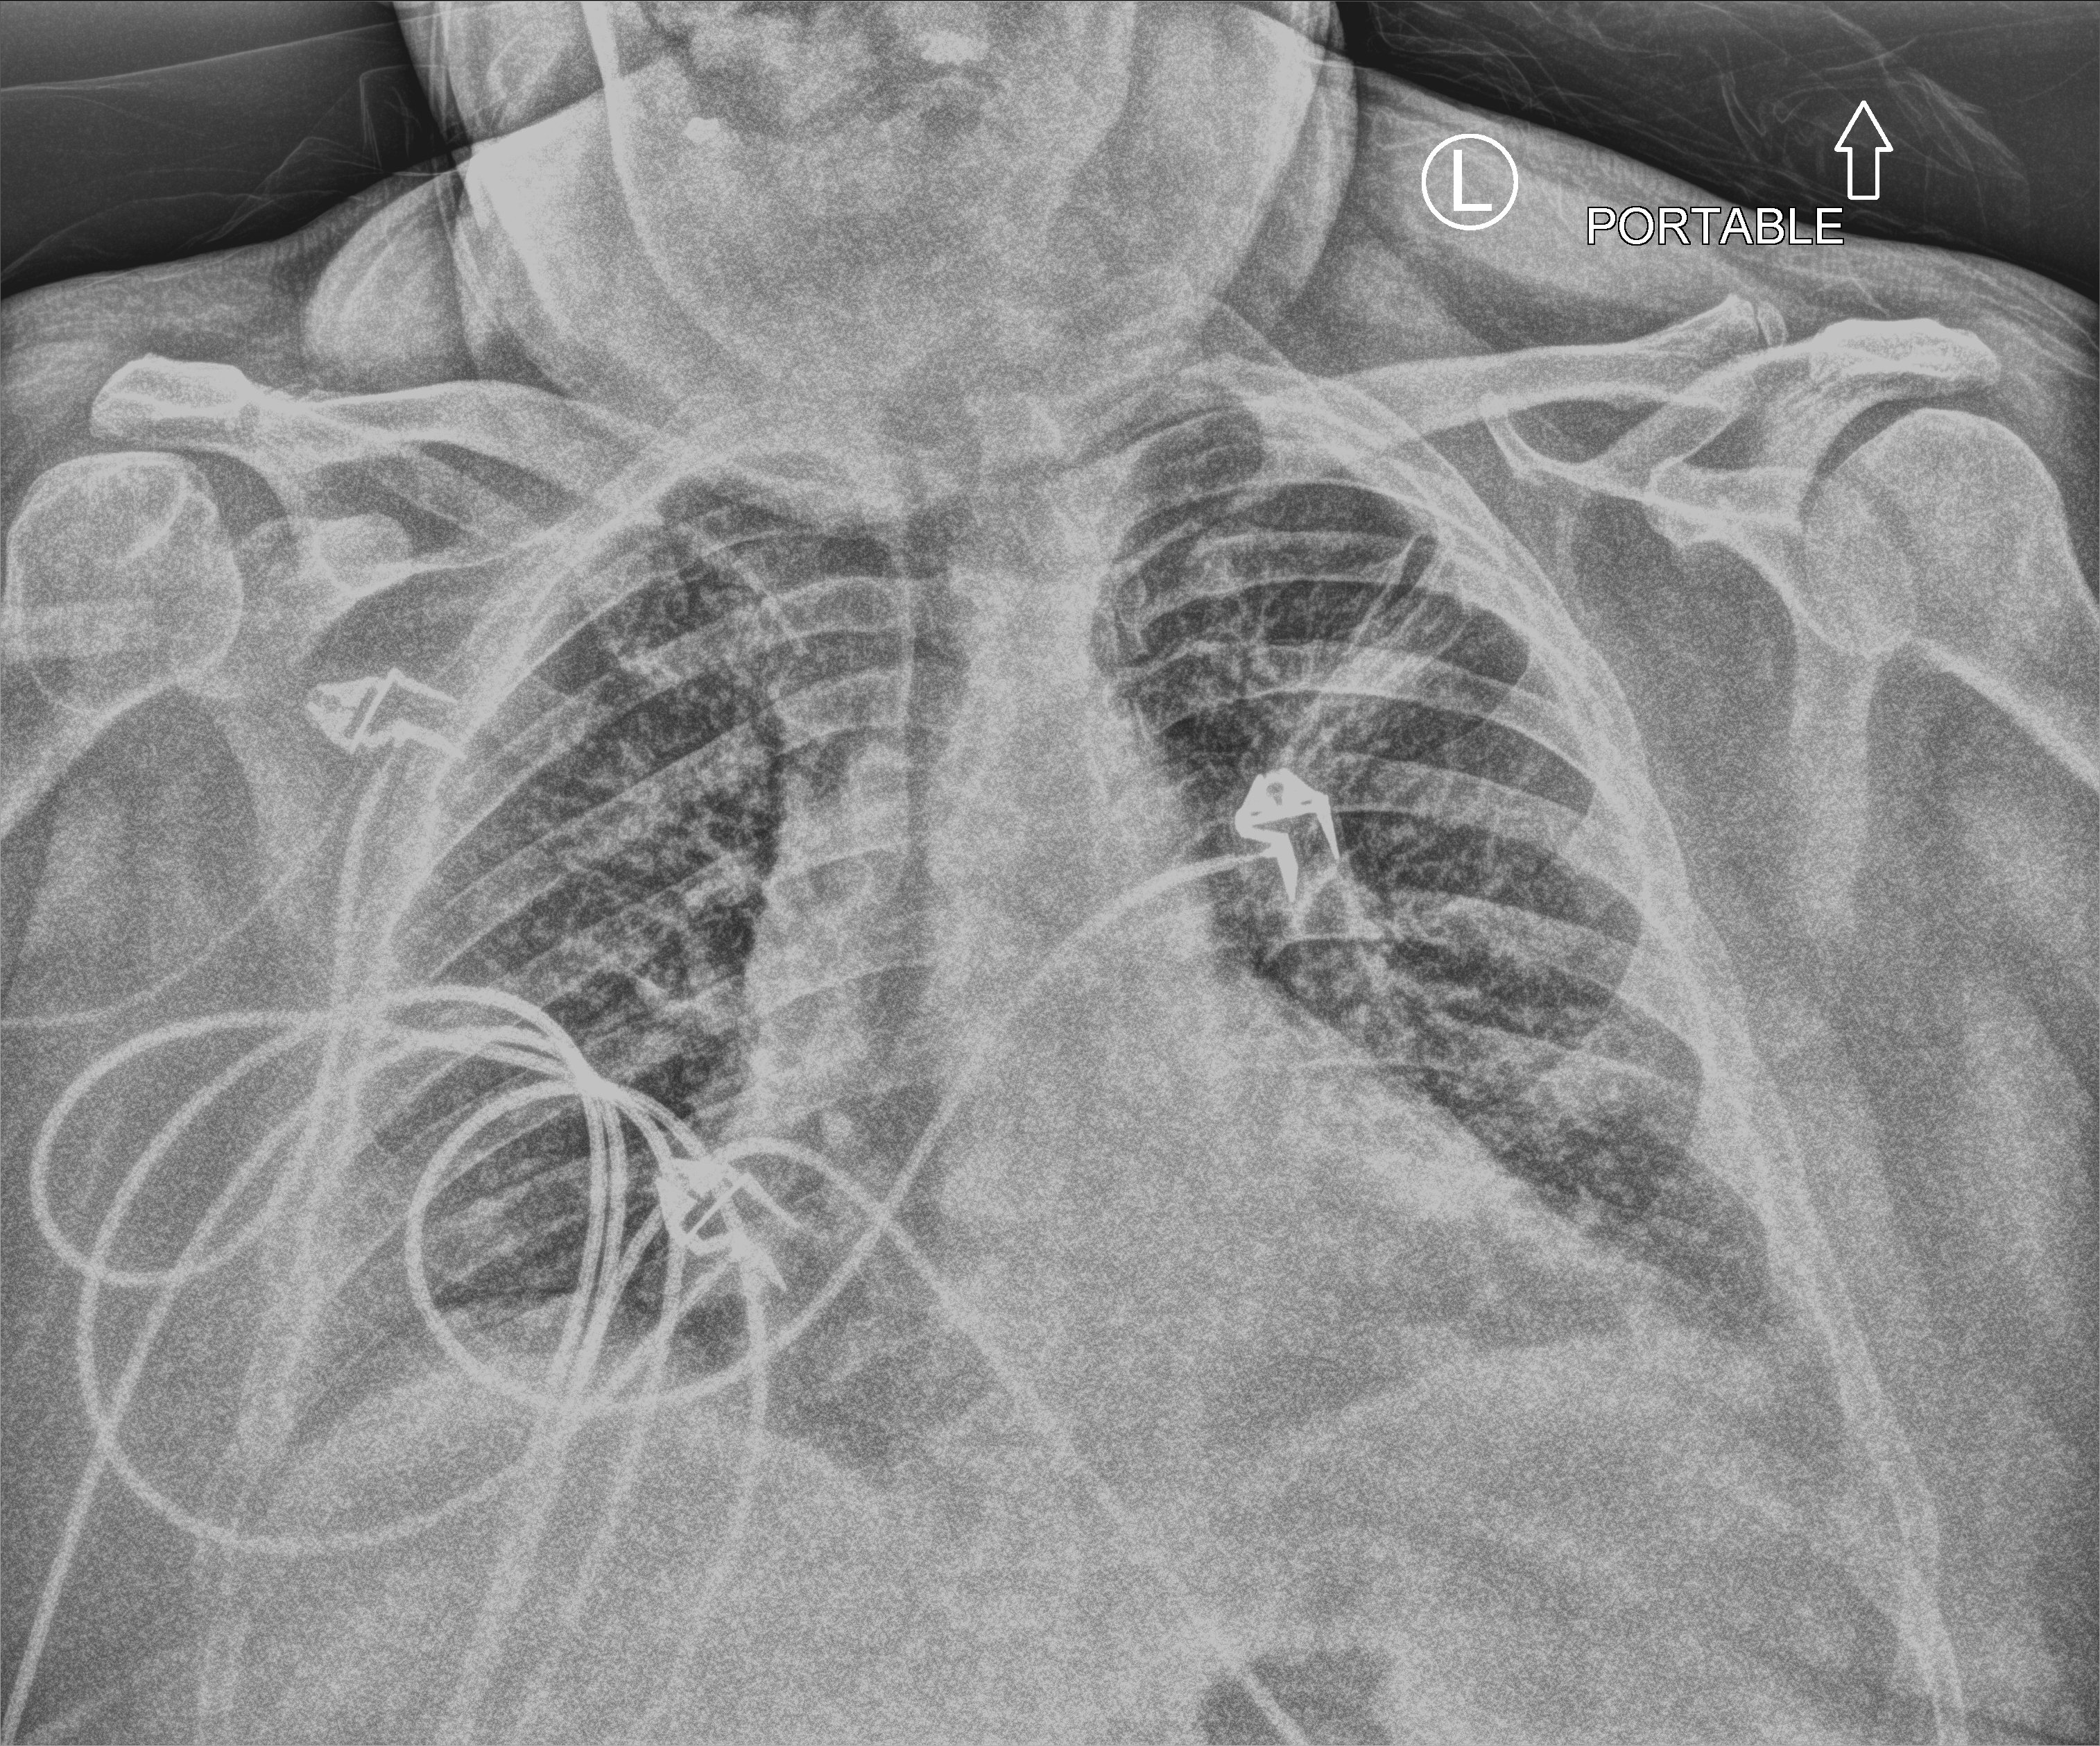
Bedside chest radiograph (computed radiography); anteroposterior (AP) projection. Male patient hospitalised with COVID-19, age 60–74 years.
From the hospital-stay record, not from the radiograph (when in the stay this image was taken is not recorded):
- mechanically ventilated during this hospital stay: no
- diabetes (admission record): yes
- smoking status (admission record): current